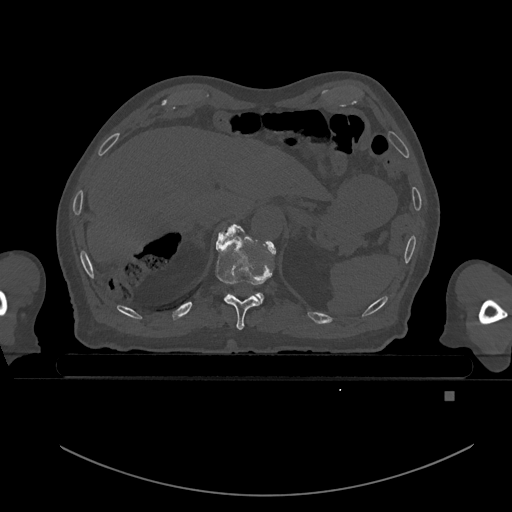
CT including the spine, one axial slice. Slice 72 of 969 in the series (ordered by position). Bone window (W 1800 / L 400 HU). 512 × 512 image matrix, field of view 456 × 456 mm. Patient: male, 82 years. Case-level facts recorded for this patient, not image findings: primary cancer: prostate.
Outlined on this slice (semi-automatic segmentation, software-assisted and operator-edited):
- T10 vertebra: bounding box (x1, y1, x2, y2) in pixels: (216, 225, 274, 330)
- T11 vertebra: (222, 227, 273, 303)